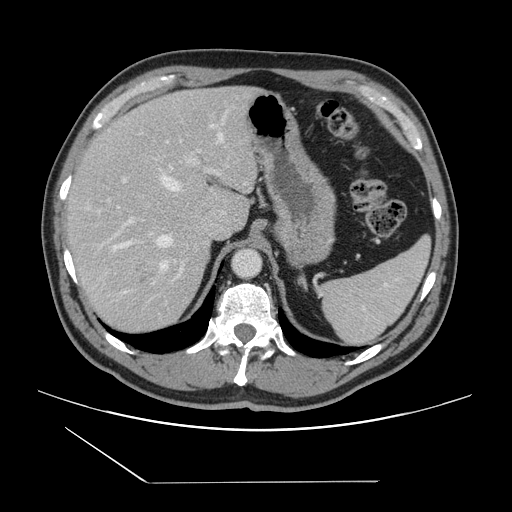
Contrast-enhanced abdominal CT, one axial slice. Slice 106 of 157 in the series (ordered by position). 120 kVp. Intravenous contrast given. Soft-tissue window (W 400 / L 40 HU). 2.5 mm slice thickness. 512 × 512 image matrix, field of view 407 × 407 mm. Male patient, age 61 years. Case-level facts recorded for this patient, not image findings: diagnosis: colorectal cancer liver metastases, imaged before liver resection; multiple liver metastases: yes; largest metastasis: 5.5 cm.
Structures marked on this image (outlined manually by an expert reader):
- hepatic veins: bounding box <98,133,224,270> (left, top, right, bottom; pixels)
- liver: <67,87,258,334>
- planned liver remnant (the part of the liver to remain after resection): <67,87,237,230>
- portal vein (with intrahepatic branches): <108,140,217,279>
- liver metastasis: <127,253,163,288>